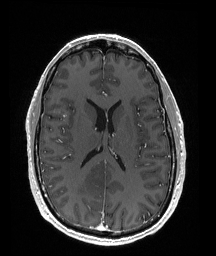
Brain MRI from a brain-tumour surgery series, one axial slice. Position 80 of 176 along the scan axis. T1-weighted post-contrast. 216 × 256 image matrix. From the clinical record (not read from this slice): histopathology: Oligodendroglioma; WHO grade: 2; IDH mutation: yes; tumour location: Right Parietal.
Annotated regions visible in this slice (outlined manually by an expert reader):
- tumour: box from (x=70, y=166) to (x=111, y=195) px